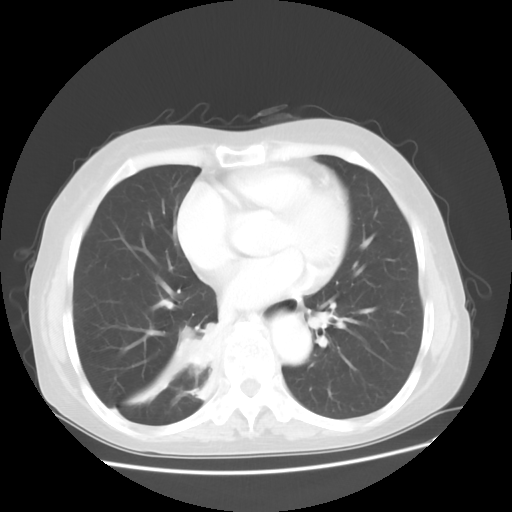
Chest CT, one axial slice. Position 17 of 48 along the scan axis. Reconstruction kernel STANDARD. 120 kVp. Lung window (W 1500 / L -600 HU). 5 mm slice thickness. 512 × 512 image matrix, field of view 360 × 360 mm. Patient: female, 63 years. Case-level facts recorded for this patient, not image findings: clinical TNM (as recorded): T2 N3 M1b; histopathological grade: G3.
Annotated regions visible in this slice (rectangle marked by the reading radiologist):
- lung tumour (recorded histology: small cell carcinoma): box from (x=179, y=319) to (x=226, y=377) px